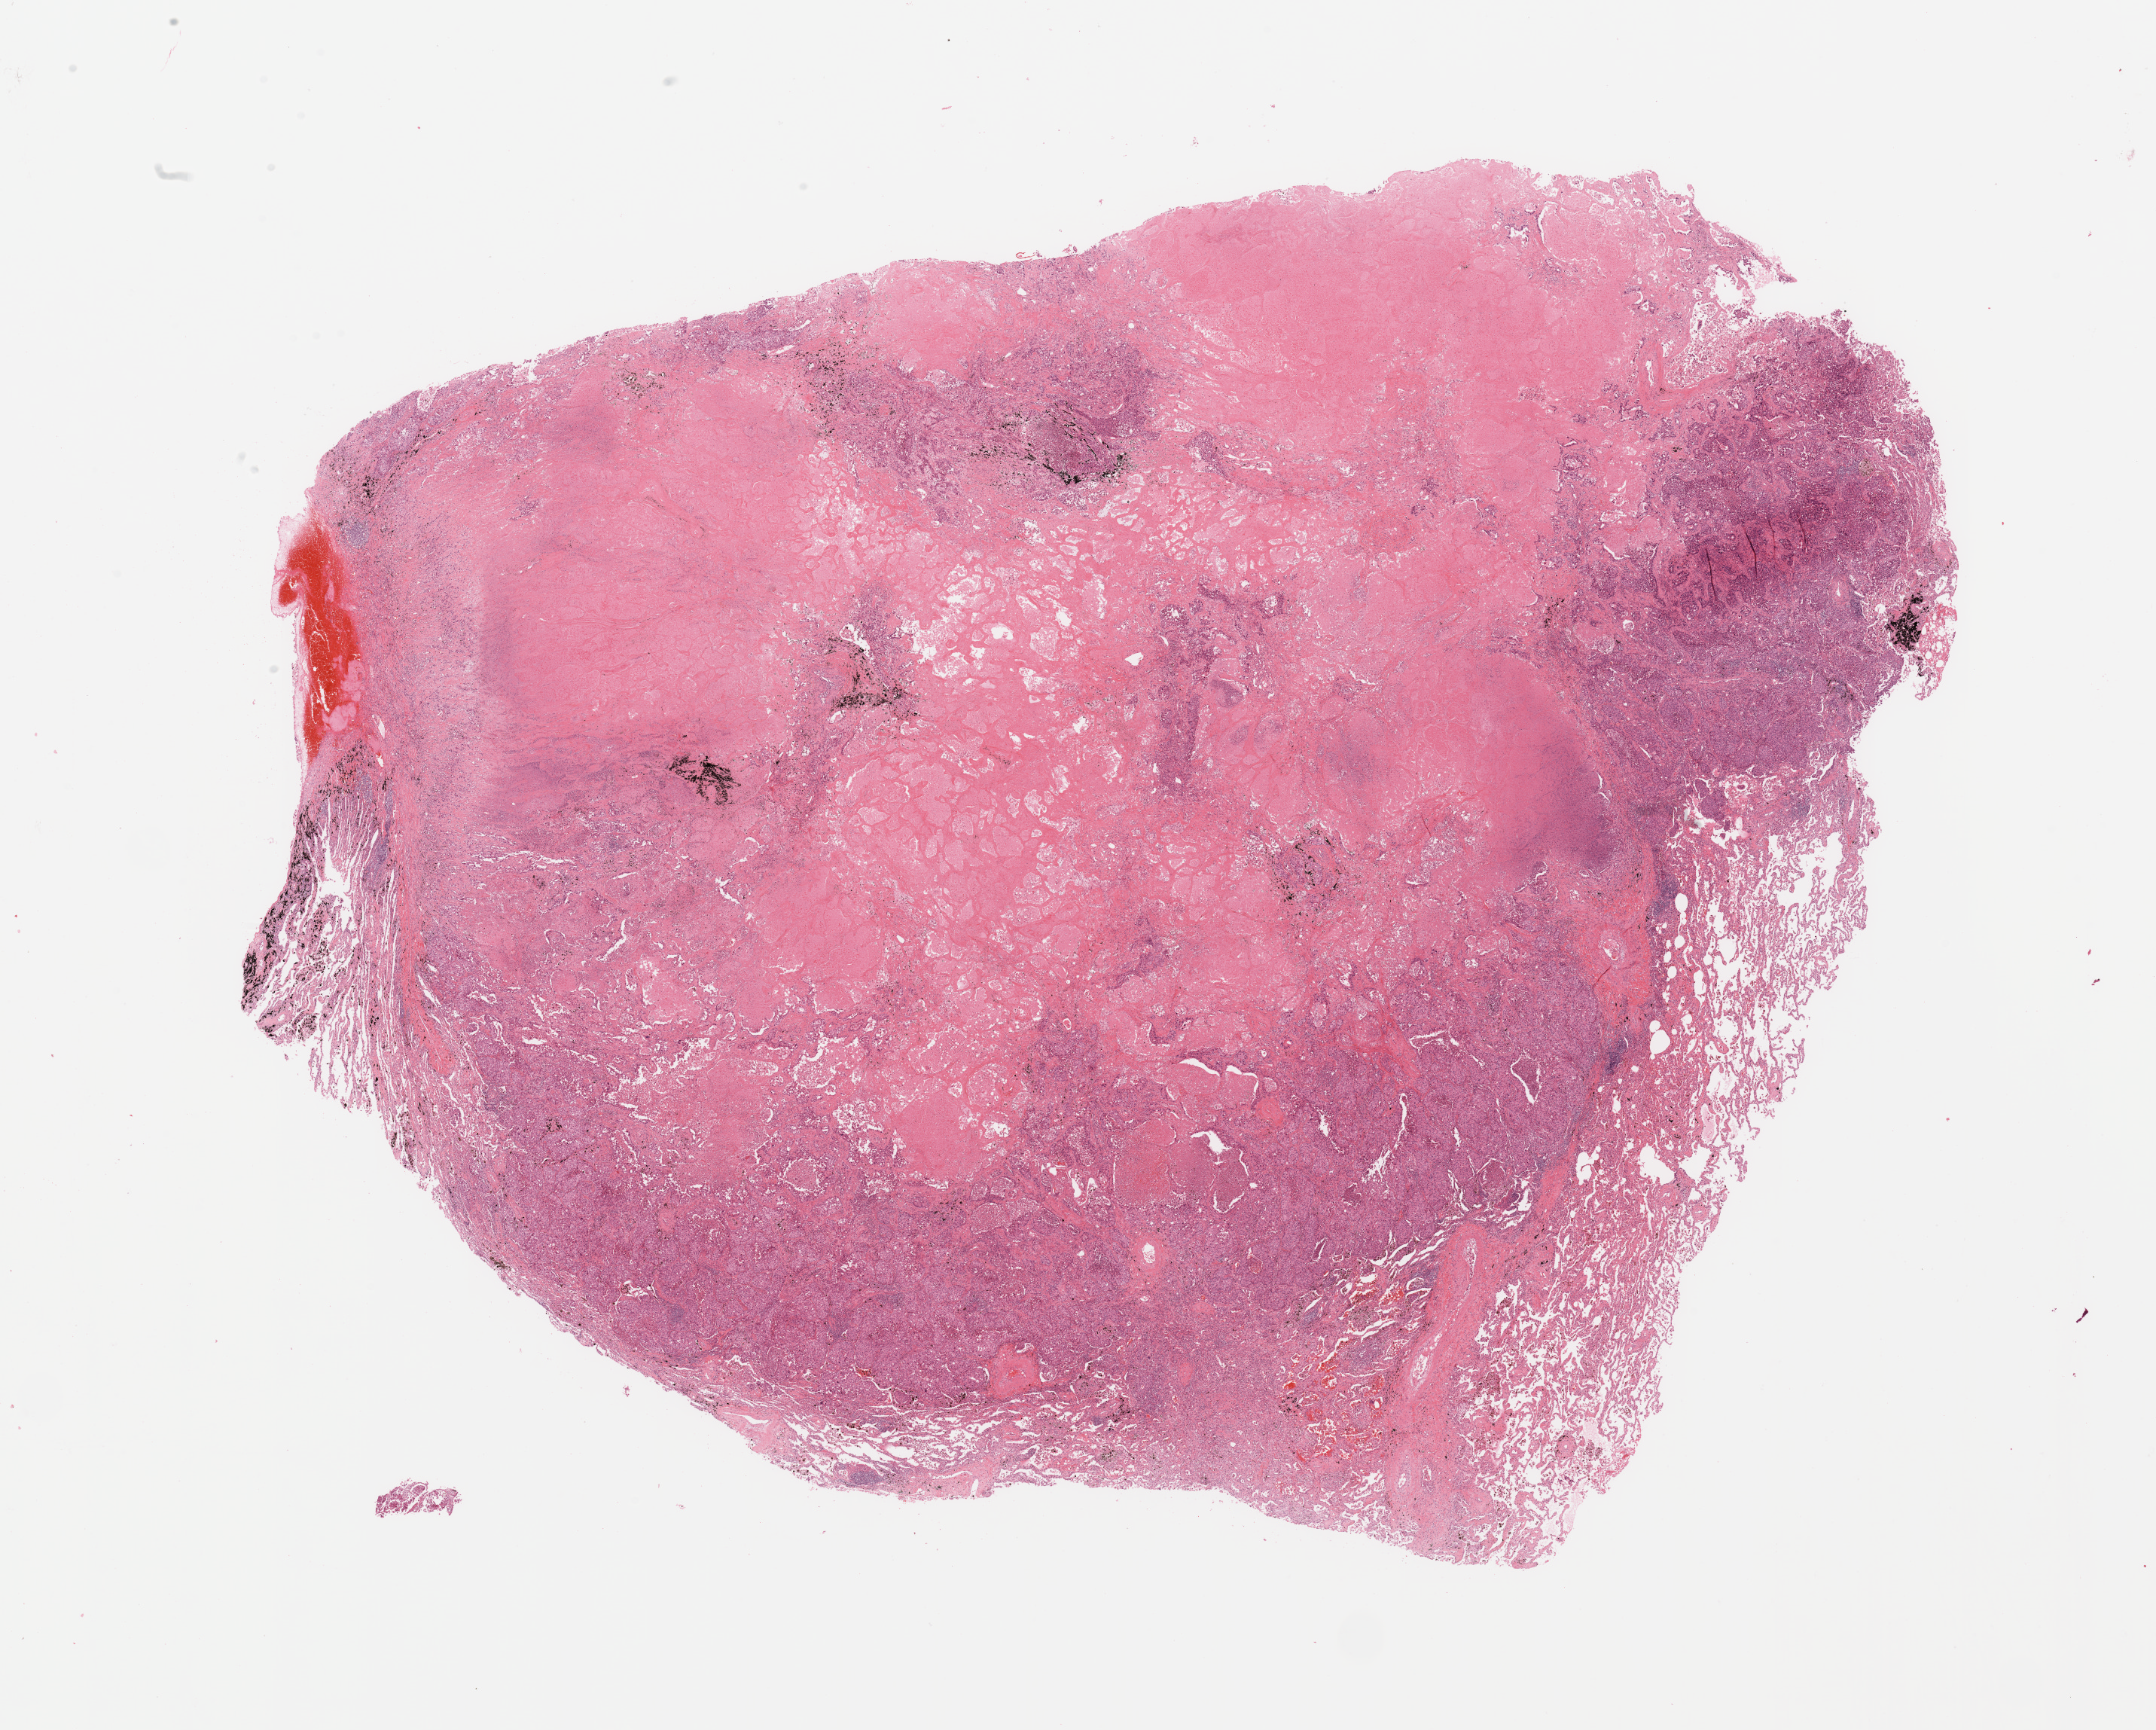
H&E whole-slide image — a low-resolution overview of the entire scanned area, about 22.6 x 18.2 mm; tumour tissue sample, lung. 64-year-old male patient.
Patient diagnosis (cohort enrolment): squamous cell carcinoma (lung).